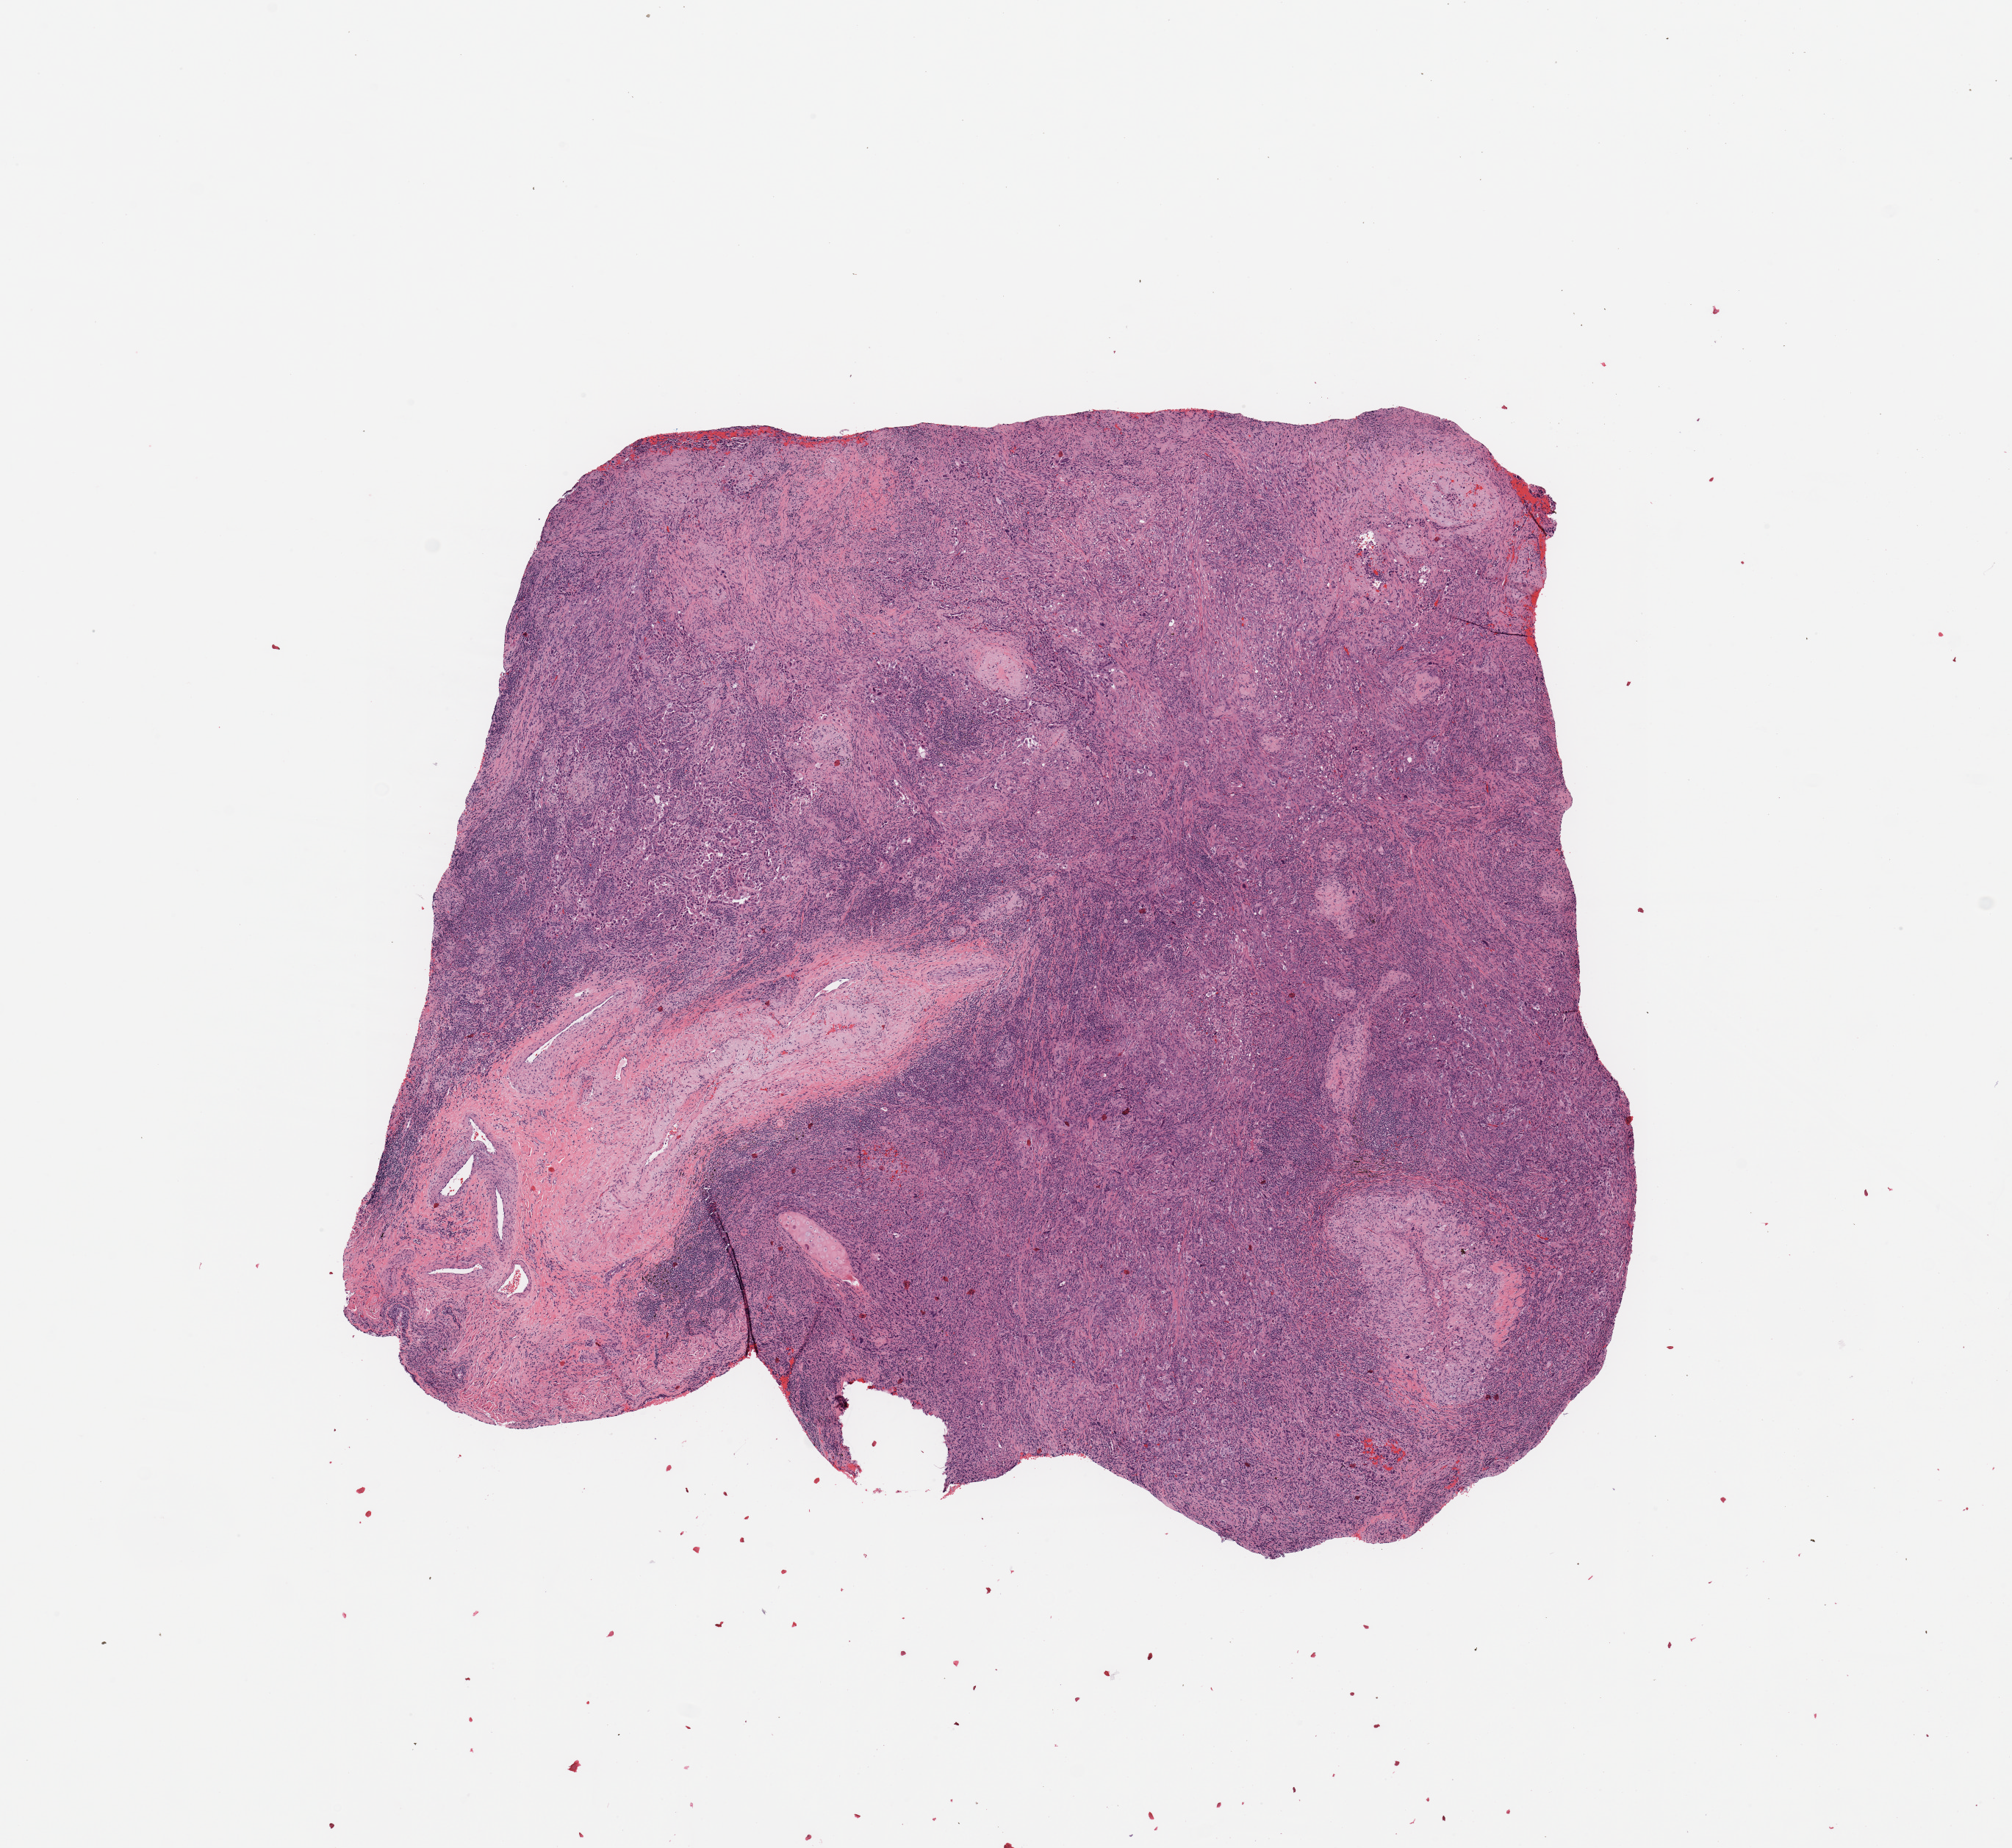
Whole-slide histology image, Hematoxylin and eosin (H&E) stained, whole scanned area (about 10.8 x 9.9 mm, slide scanned at 20x) shown as a low-resolution overview, tumour tissue sample, sampled site: lung. 77-year-old male patient. Histologic grade: G3 (poorly differentiated). Pathologist review of this section (percent, as recorded): tumour nuclei 70%, necrosis 0%.
• primary tumour site (as recorded): right lower lobe
• histologic diagnosis: Adenocarcinoma, NOS
• AJCC pathologic stage: IB